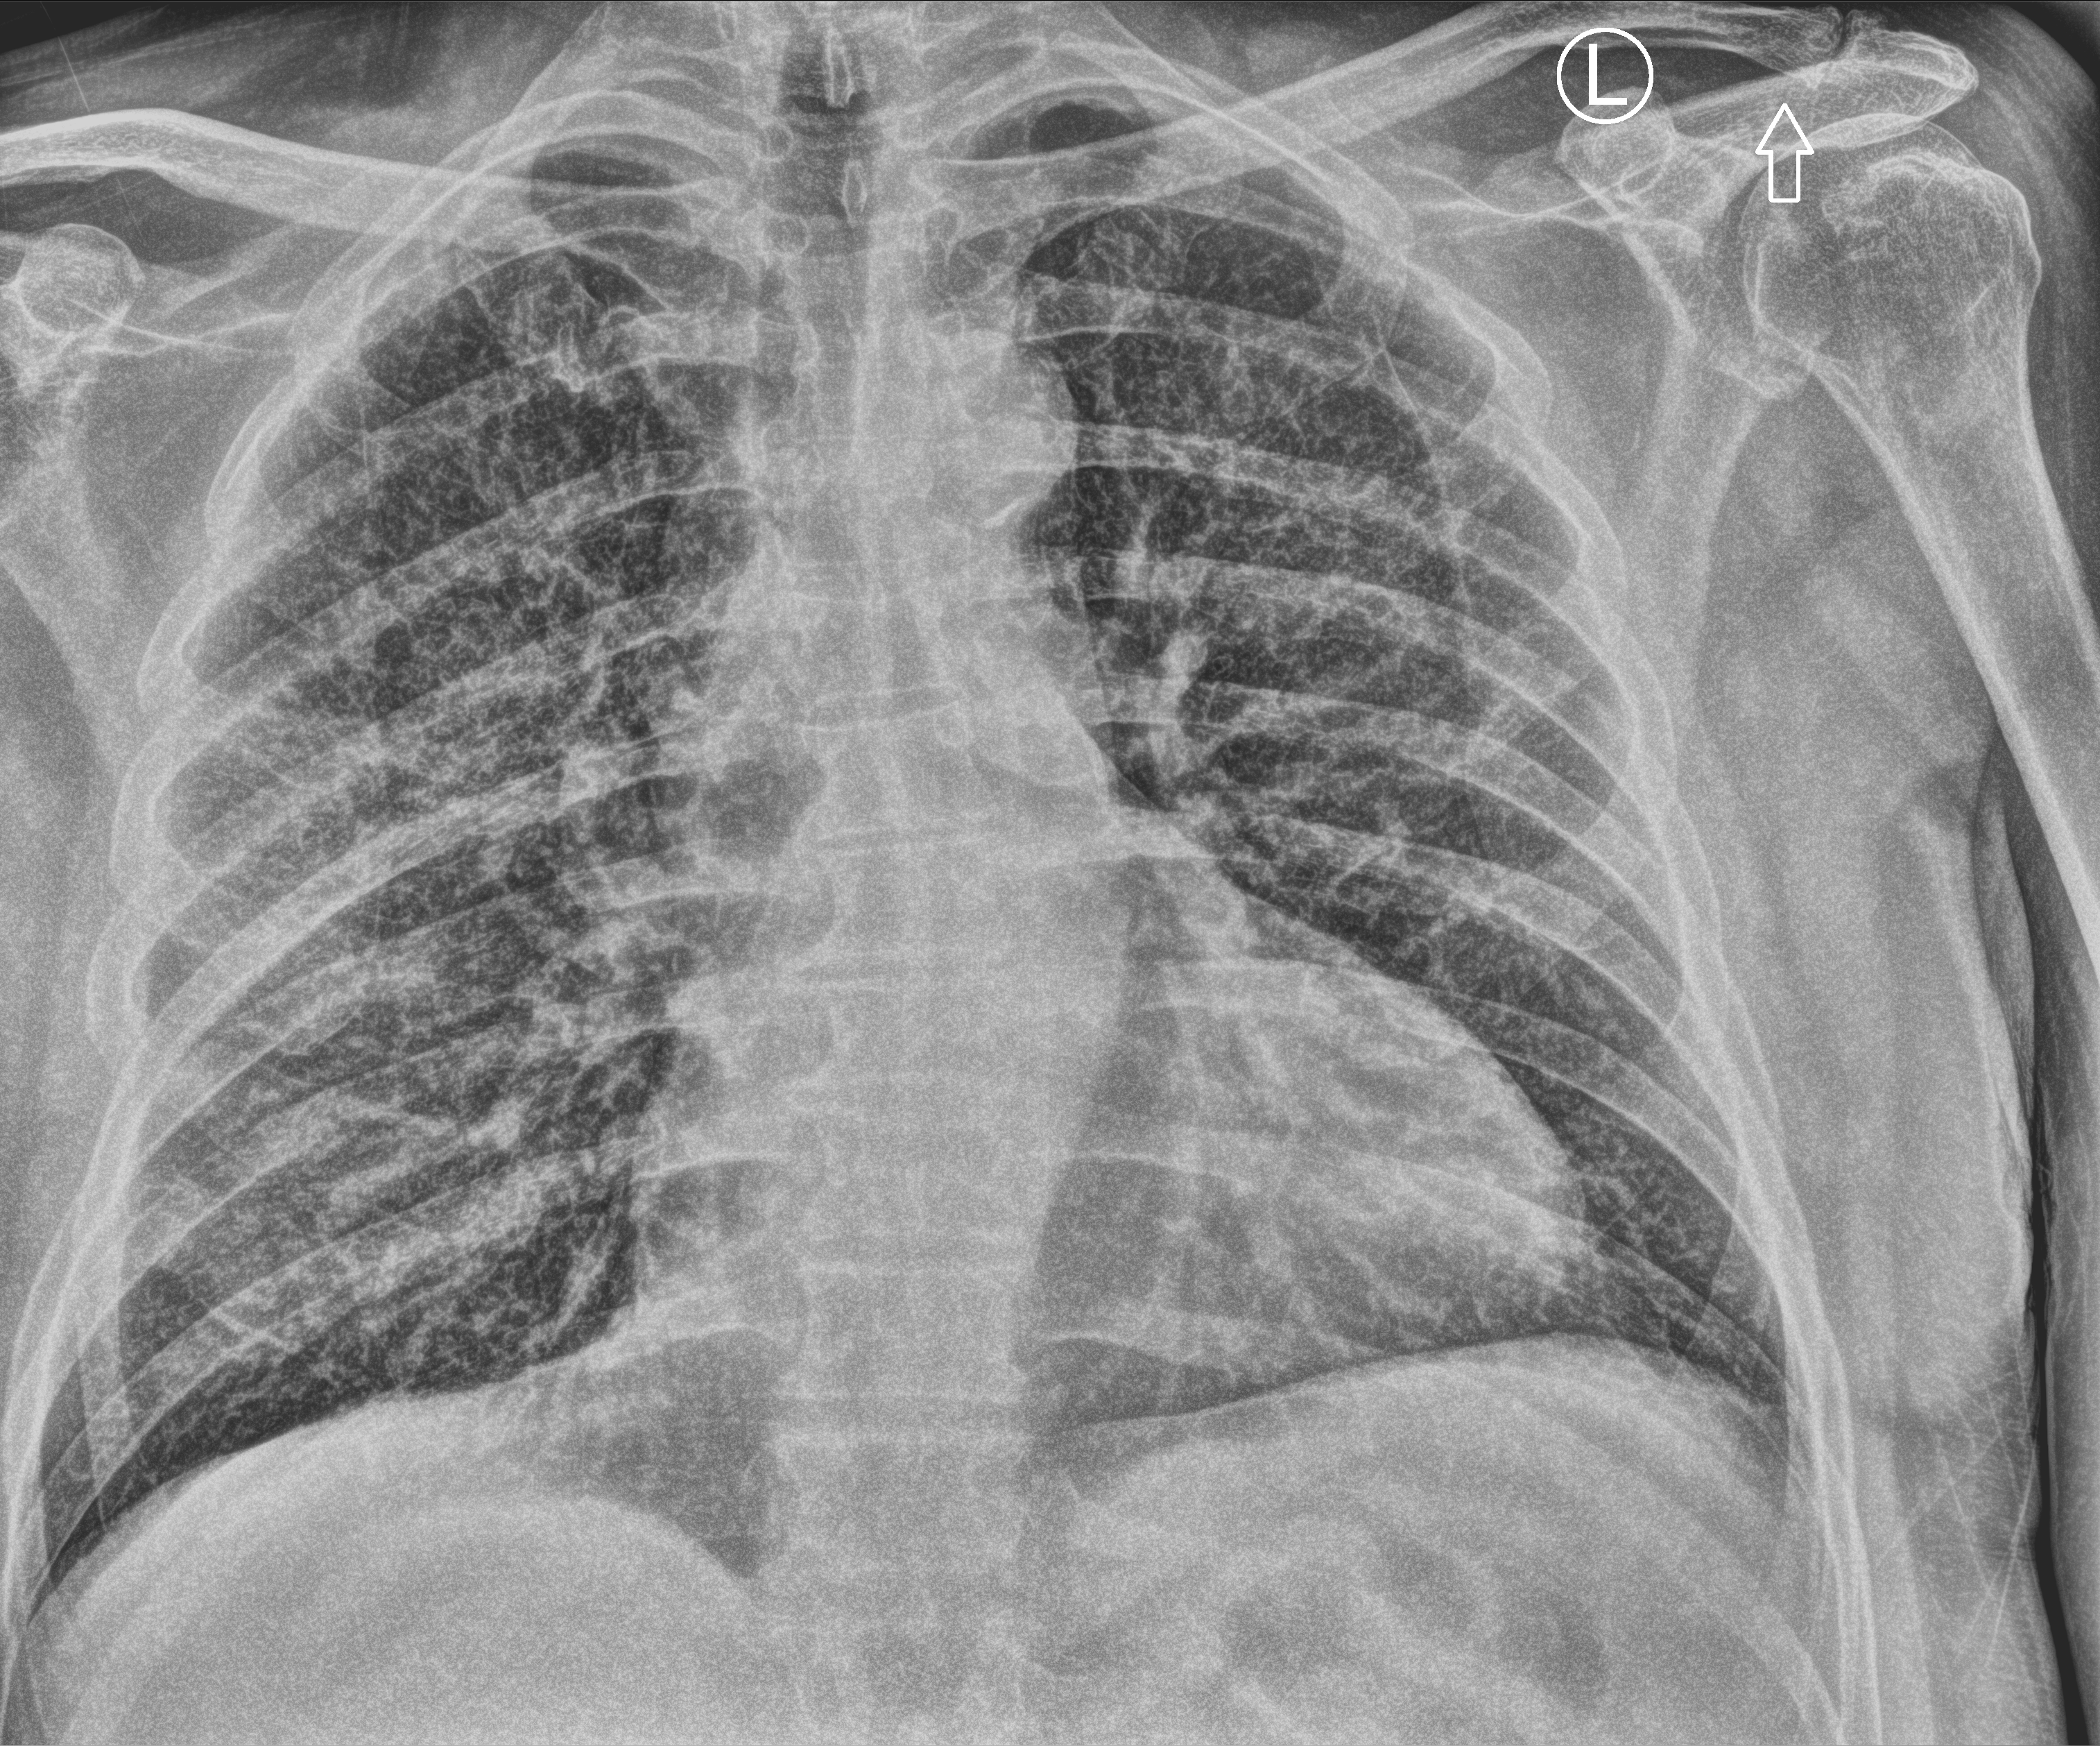
Chest X-ray (portable); anteroposterior (AP) projection. Patient hospitalised with COVID-19; male, aged 60–74 years.
Admission-level facts for this patient (not findings on this image; timing relative to this image not recorded):
- admitted to intensive care during this hospital stay: no
- length of hospital stay: 2 days